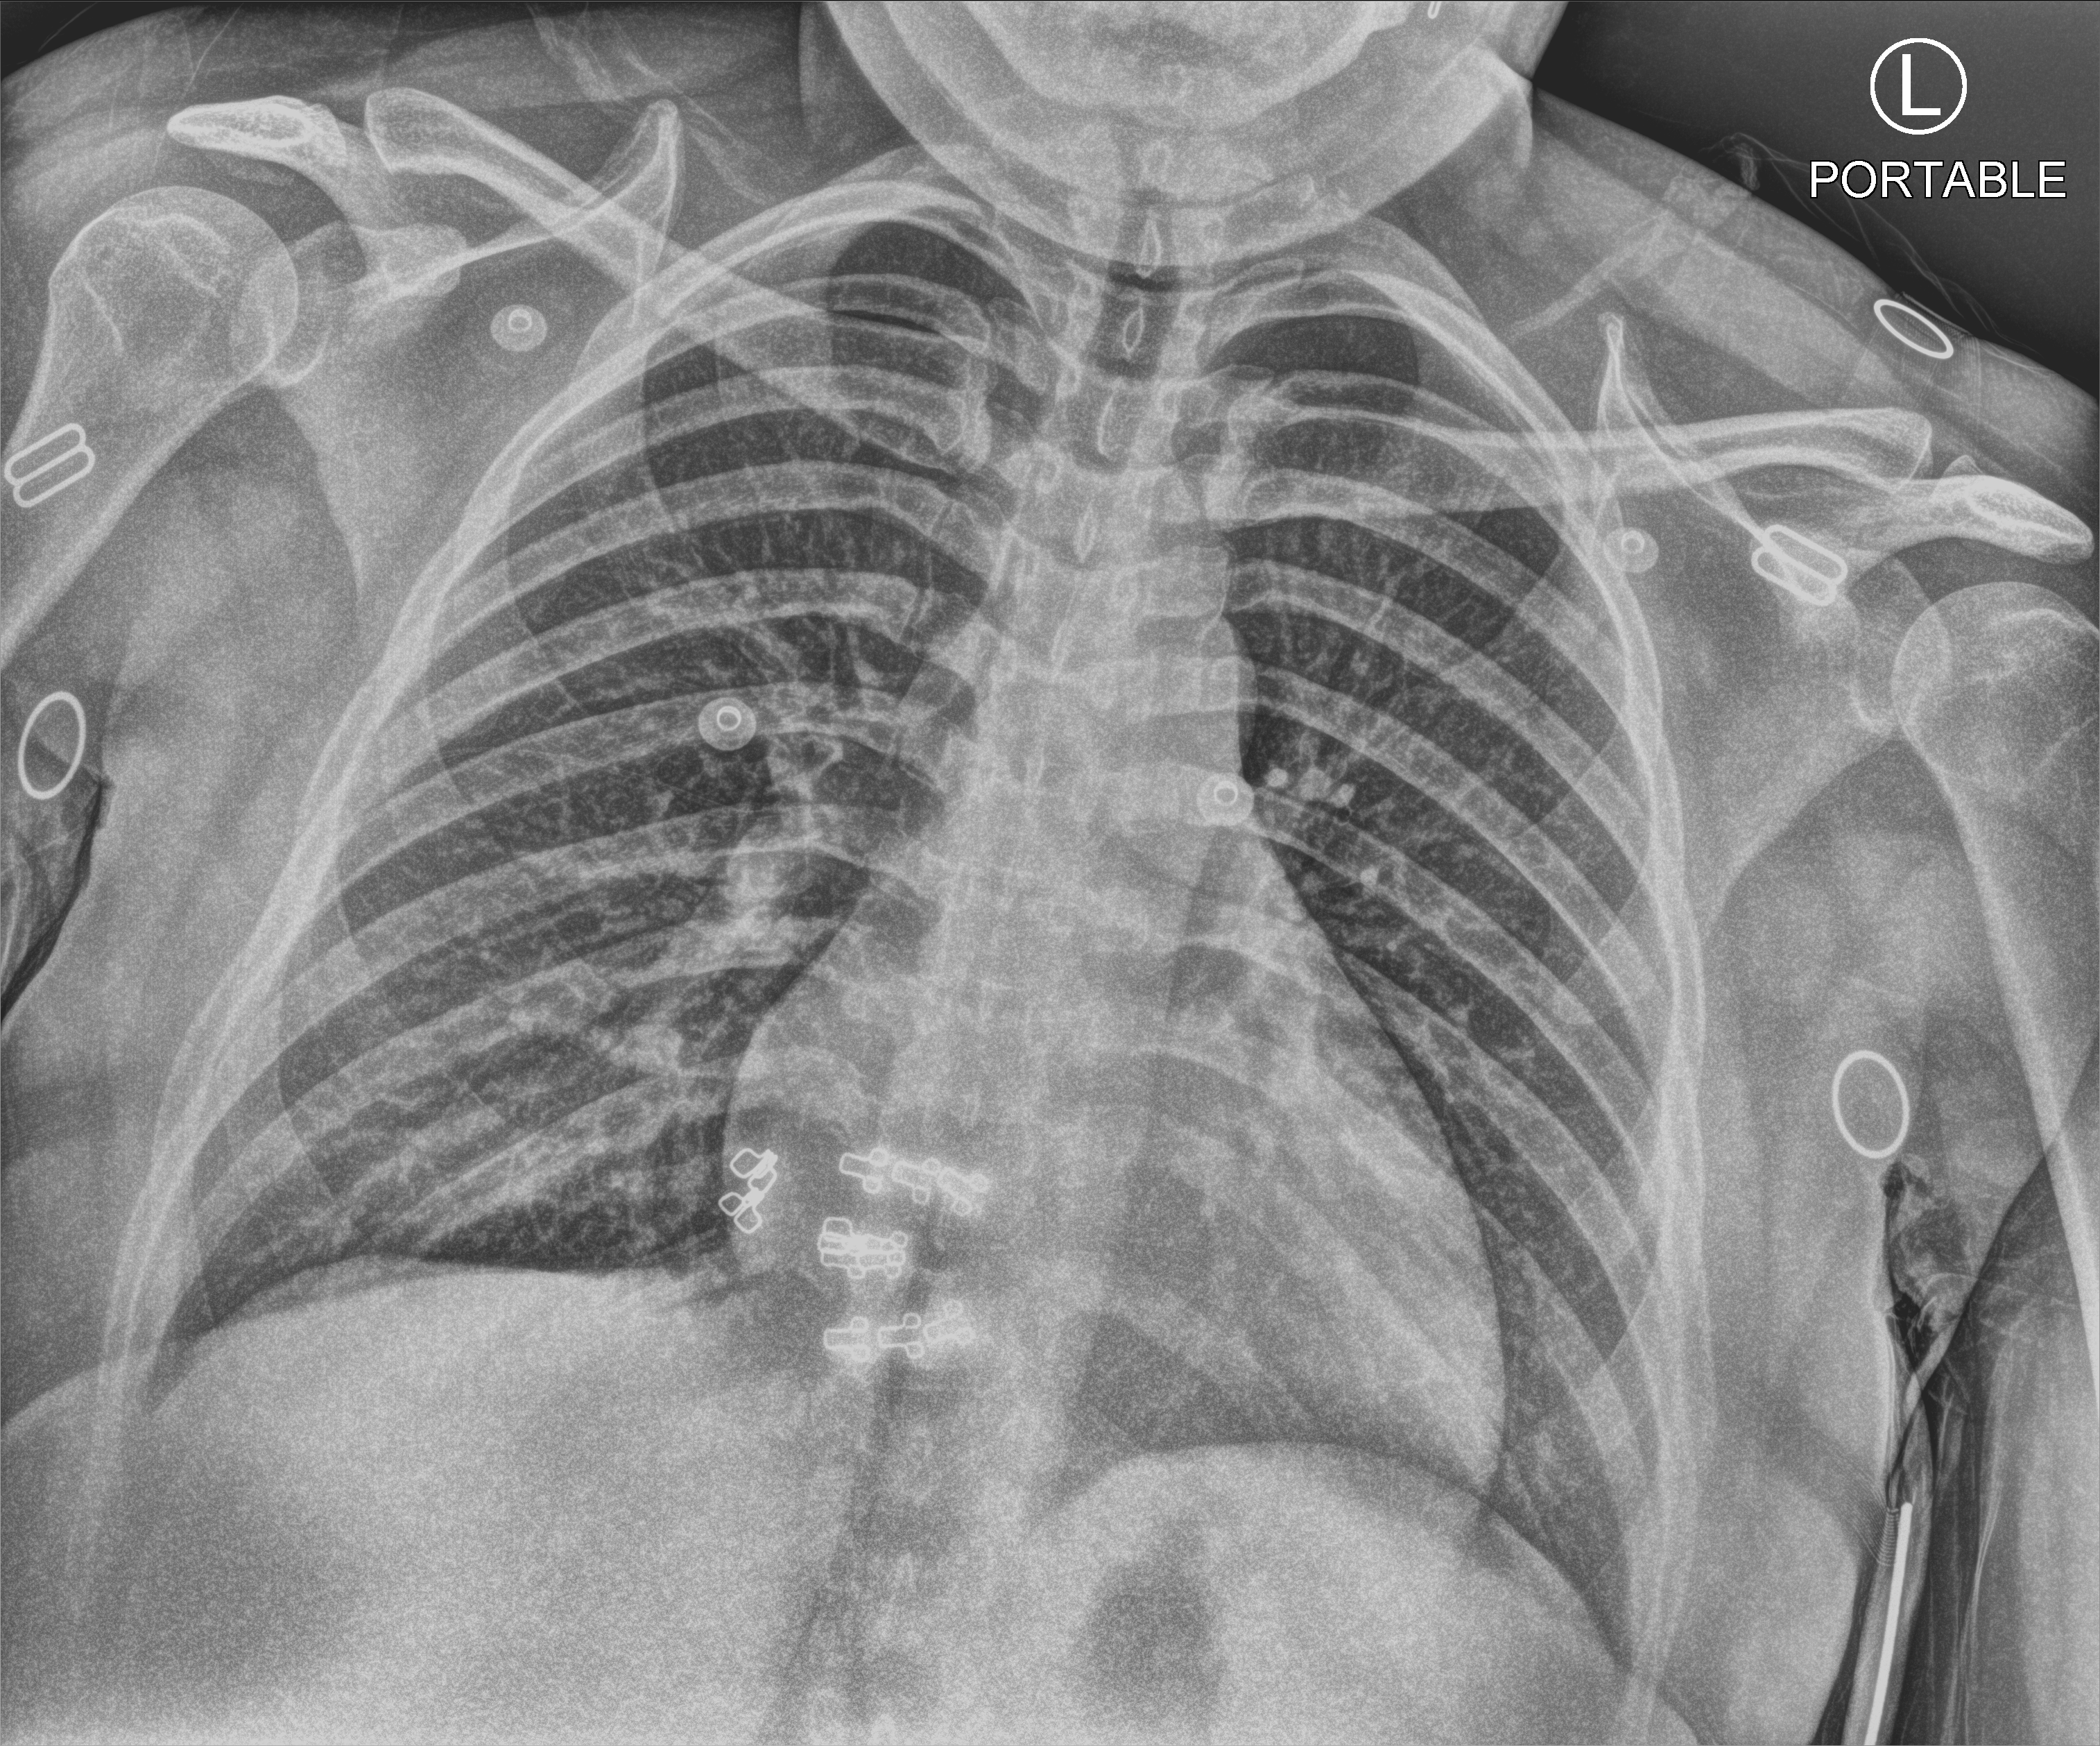
Chest X-ray (portable). Female patient hospitalised with COVID-19, age 18–59 years.
From the hospital-stay record, not from the radiograph (when in the stay this image was taken is not recorded): mechanically ventilated during this hospital stay: no; admitted to intensive care during this hospital stay: no.